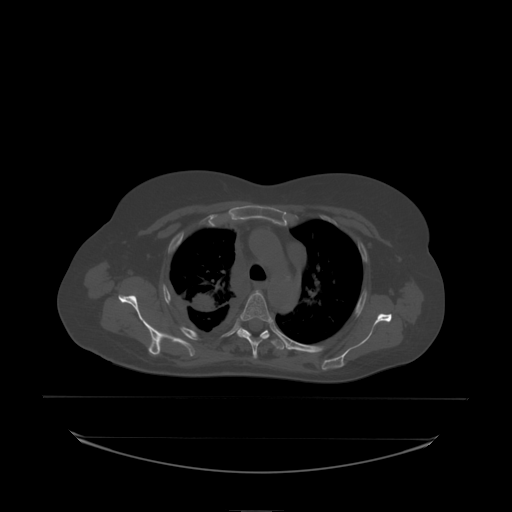
CT including the spine, one axial slice. Slice 164 of 242 in the series (ordered by position). Bone window (W 1800 / L 400 HU). 2.5 mm slice thickness. 512 × 512 image matrix, field of view 500 × 500 mm. Patient: female, 53 years. From the clinical record (not read from this slice): primary cancer: lung; vertebrae with lytic lesions (as recorded): T7, L1.
Outlined on this slice (semi-automatic segmentation, software-assisted and operator-edited):
- T4 vertebra: bounding box (x1, y1, x2, y2) in pixels: (238, 291, 274, 338)
- T5 vertebra: (237, 328, 270, 338)